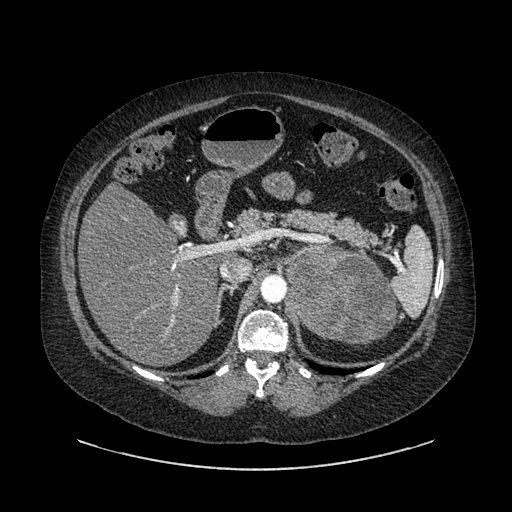
Contrast-enhanced abdominal CT, one axial slice; slice 579 of 769 in the series (ordered by position); reconstruction kernel SOFT; intravenous contrast given; soft-tissue window (W 400 / L 40 HU); 512 × 512 image matrix, field of view 460 × 460 mm. Patient: female, 61 years. Case-level facts recorded for this patient, not image findings: diagnosis: adrenocortical carcinoma; tumour side: left adrenal; tumour size at pathology: 13 cm; Ki-67 index: 79 %; stage (as recorded): 2.
Structures marked on this image (semi-automatic segmentation, software-assisted and operator-edited):
- mass: bounding box [x1, y1, x2, y2] px = [287, 246, 393, 344]